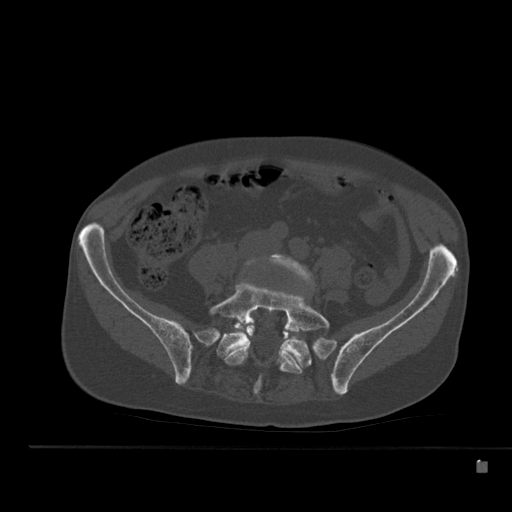
CT including the spine, one axial slice. Slice 124 of 517 in the series (ordered by position). Reconstruction kernel Br40s. 120 kVp. Bone window (W 1800 / L 400 HU). 1.5 mm slice thickness. 512 × 512 image matrix, field of view 408 × 408 mm. Male patient, age 70 years. Case-level facts recorded for this patient, not image findings: primary cancer: renal; vertebrae with lytic lesions (as recorded): T4, T6, T10, T12, L3, L4, L5.
Structures marked on this image (semi-automatic segmentation, software-assisted and operator-edited):
- L4 vertebra: bounding box [x1, y1, x2, y2] px = [244, 254, 315, 286]
- L5 vertebra: [209, 283, 330, 395]